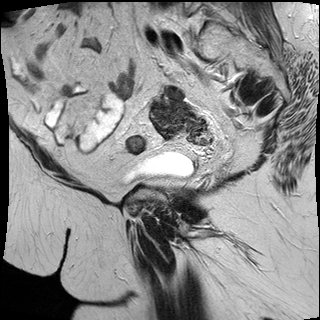
Pelvic MRI for cervical cancer, one sagittal slice; position 12 of 32 along the scan axis; T2-weighted; 1.5 T; TE 87 ms, TR 3063.4 ms; 4 mm slice thickness; 320 × 320 image matrix. Female patient, age 53 years.
Structures marked on this image (expert manual segmentation):
- uterus and cervix: bounding box [x1, y1, x2, y2] px = [150, 99, 196, 137]